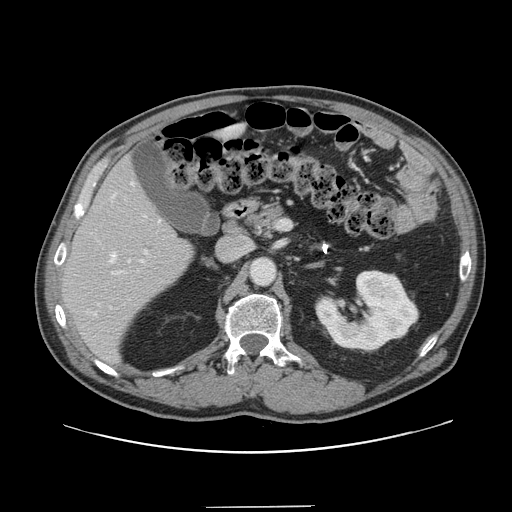
Contrast-enhanced abdominal CT, one axial slice; position 78 of 139 along the scan axis; 120 kVp; intravenous contrast given; soft-tissue window (W 400 / L 40 HU); 512 × 512 image matrix, field of view 397 × 397 mm. Male patient, age 64 years. Case-level facts recorded for this patient, not image findings: diagnosis: colorectal cancer liver metastases, imaged before liver resection.
Structures marked on this image (manually delineated by an expert):
- hepatic veins: bounding box [x1, y1, x2, y2] px = [94, 182, 161, 315]
- liver: [63, 161, 193, 363]
- planned liver remnant (the part of the liver to remain after resection): [63, 160, 193, 361]
- portal vein (with intrahepatic branches): [111, 250, 148, 274]